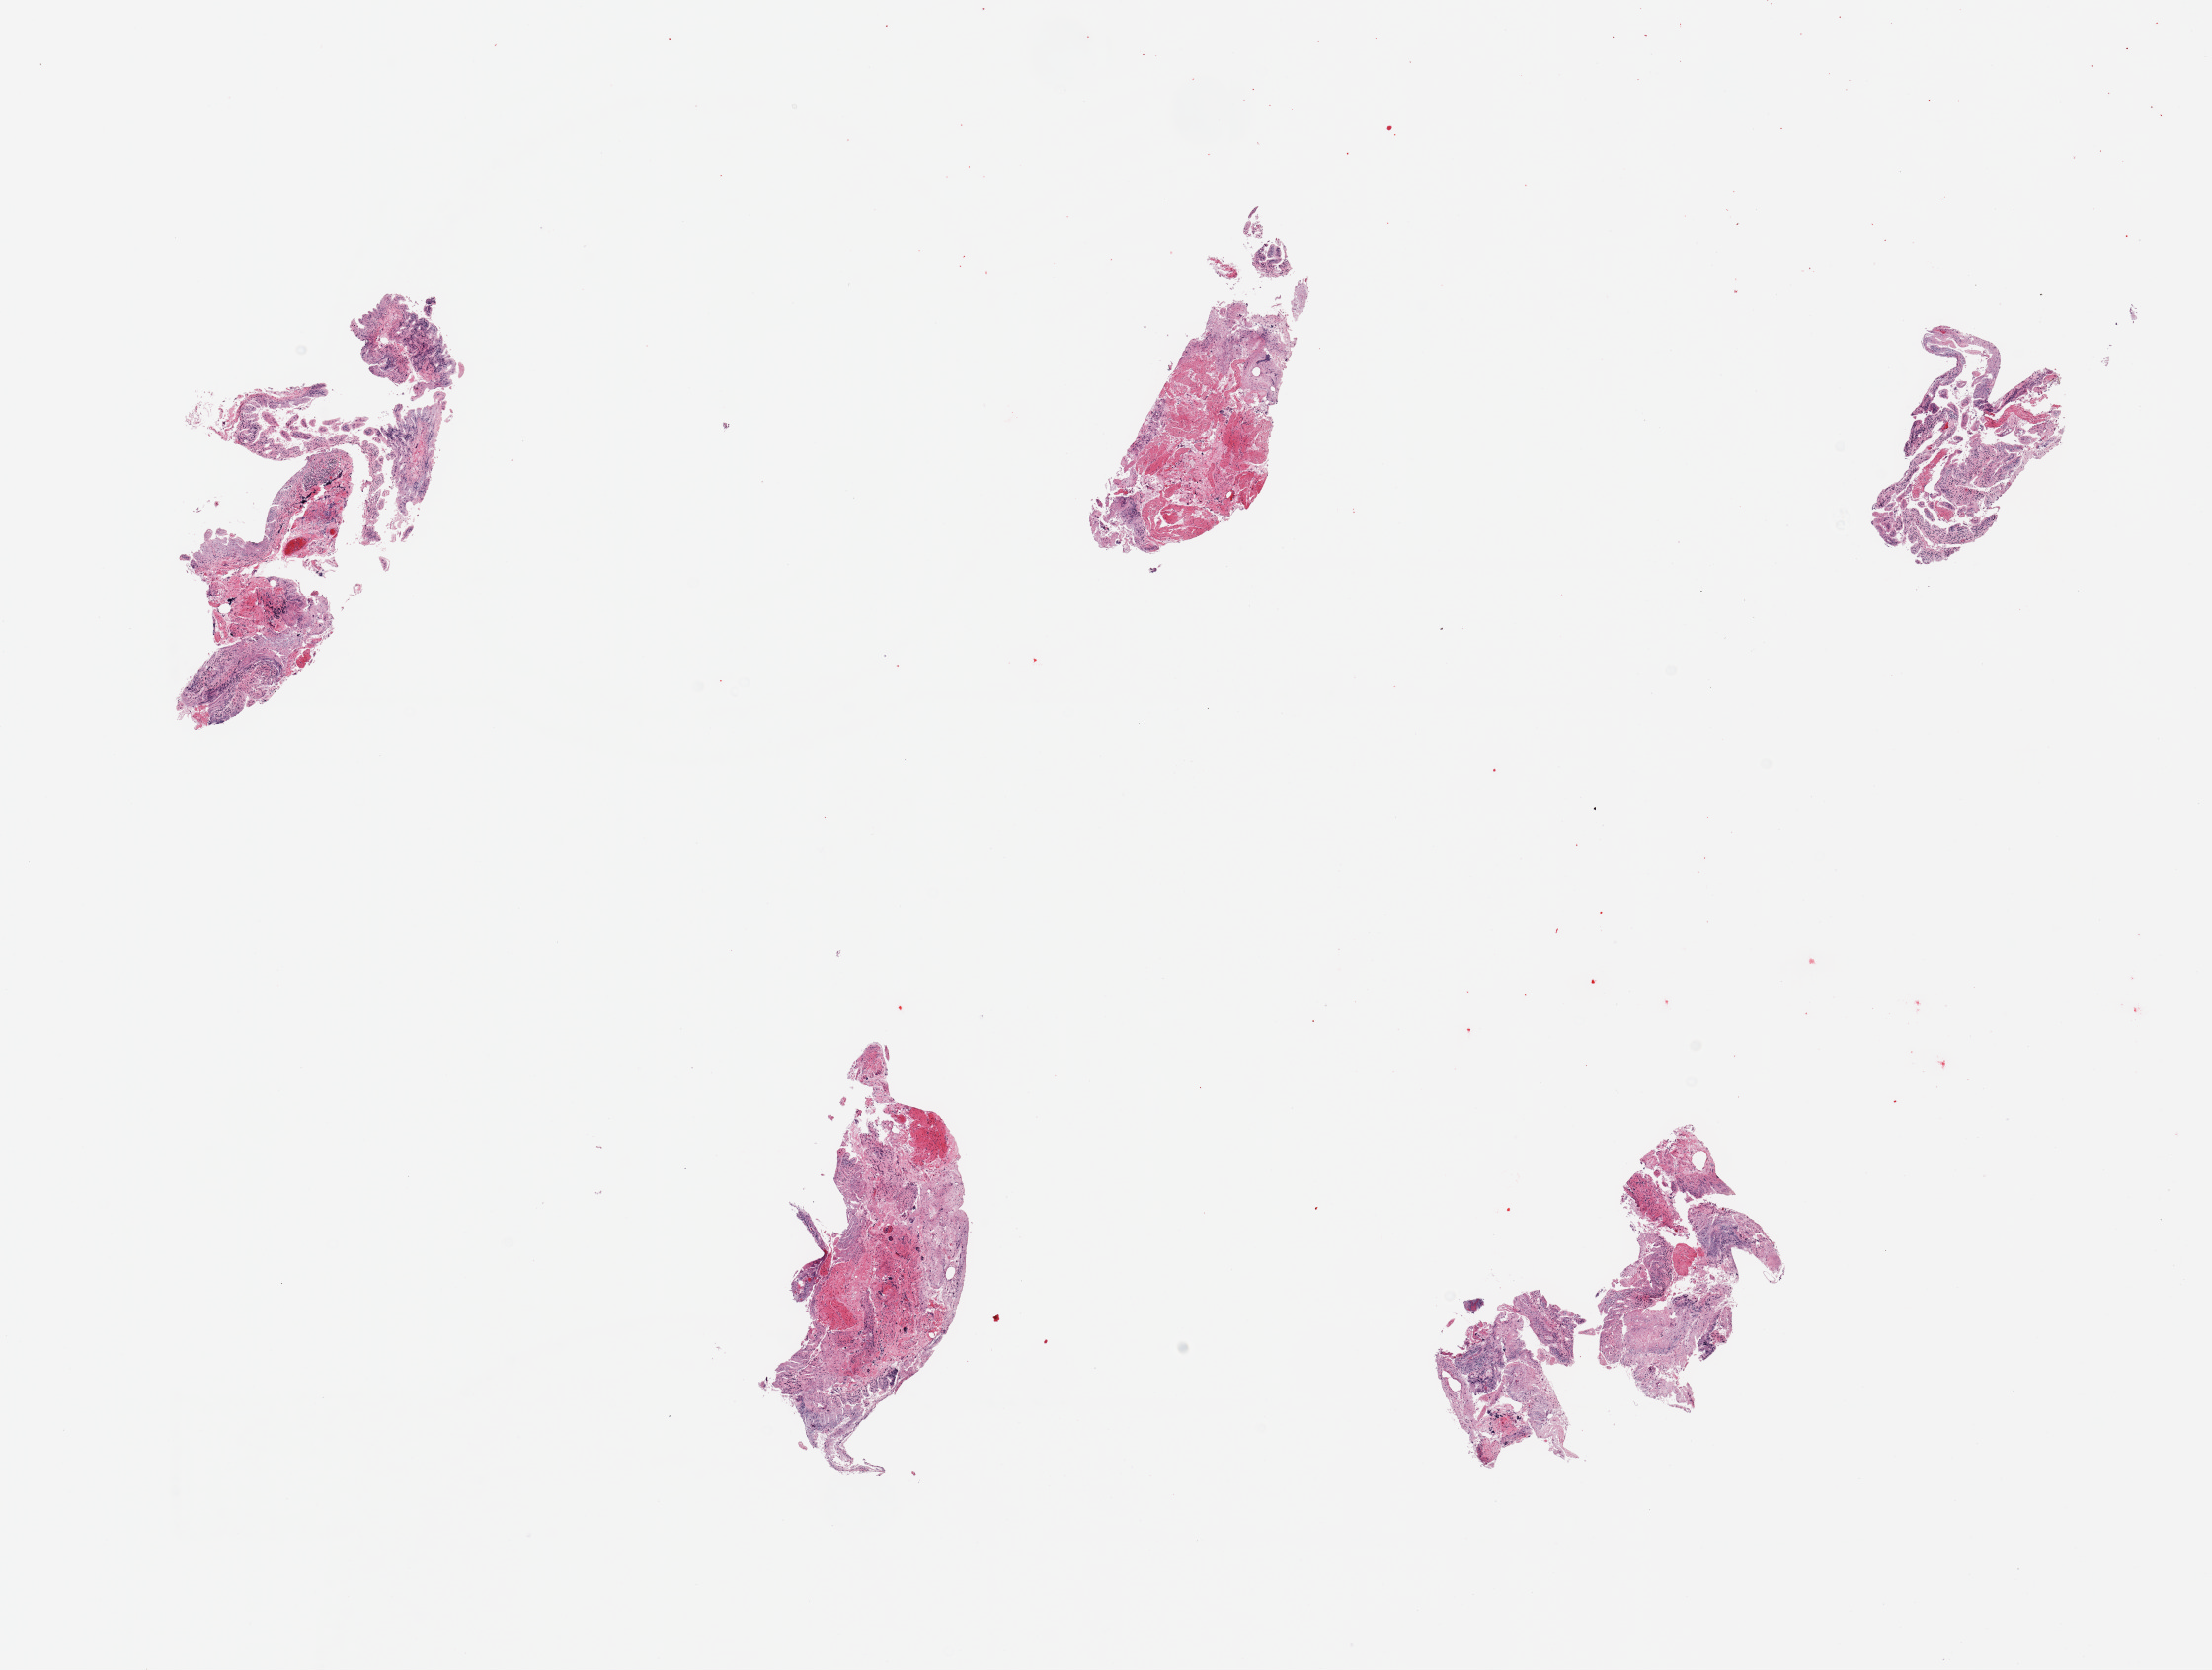
H&E whole-slide image, brightfield, low-resolution overview of the scanned area, about 17.7 x 13.4 mm; PAXgene-fixed paraffin-embedded (PFPE) section; target tissue: ileum; tissue donor sample. Donor: male.
Review note (as recorded): 6 pieces, autolyzed mucosa; insufficient target lymphoid aggregates.